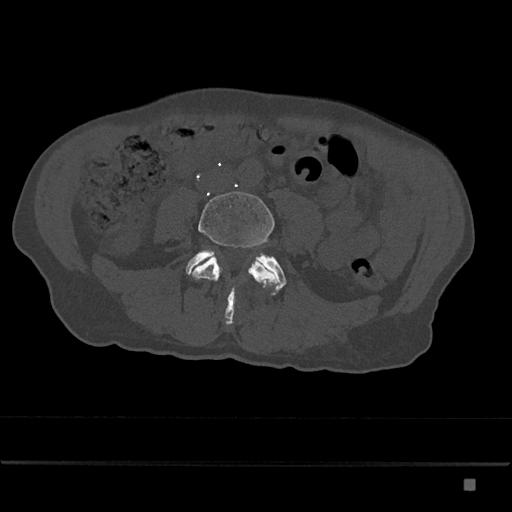
CT including the spine, one axial slice; slice 318 of 797 in the series (ordered by position); 120 kVp; bone window (W 1800 / L 400 HU); 0.5 mm slice thickness; 512 × 512 image matrix. Male patient, age 72 years. Case-level facts recorded for this patient, not image findings: primary cancer: prostate.
Structures marked on this image (semi-automatic segmentation, software-assisted and operator-edited):
- L4 vertebra: box from (x=190, y=191) to (x=277, y=305) px
- L5 vertebra: (x=185, y=250)–(x=286, y=324)